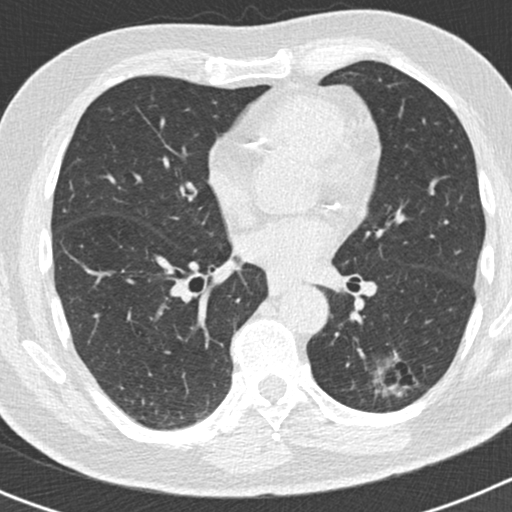
Axial slice from a low-dose chest CT screening exam, second screening round (one year after baseline), lung window (W 1500 / L -600 HU), 2 mm slice thickness, standard (soft-tissue) reconstruction kernel (B30f), 120 kVp, 512 × 512 image matrix. Male participant, aged 66 years at enrolment.
Expert-annotated lung lesion, bounding box [x1, y1, x2, y2] px = [351, 337, 412, 406]. Screening reader's record for this exam (one nodule recorded; not confirmed to be the boxed lesion): non-calcified nodule or mass ≥4 mm, left lower lobe, 50 × 33 mm, smooth margins, pre-existing on the prior screen: yes; interval growth: yes. Lung cancer was diagnosed 440 days after this screen (after the third annual screen): adenocarcinoma, NOS, left lower lobe, poorly differentiated (G3), stage IB (AJCC 6th edition), 38 mm at pathology.